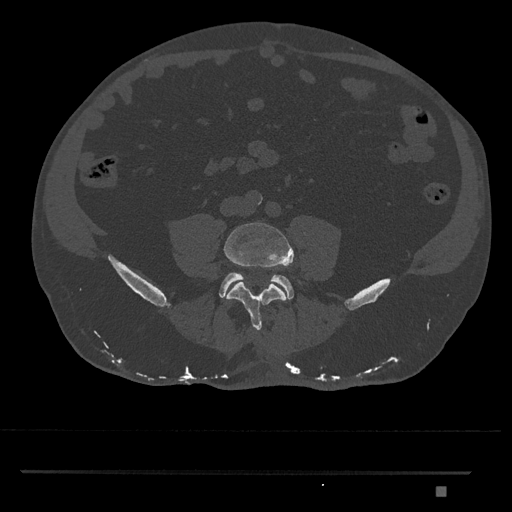
CT including the spine, one axial slice. Bone window (W 1800 / L 400 HU). 0.5 mm slice thickness. 512 × 512 image matrix. Patient: male, 65 years. Case-level facts recorded for this patient, not image findings: primary cancer: prostate.
Structures marked on this image (semi-automatically segmented with operator editing):
- L4 vertebra: bounding box <224,222,294,331> (left, top, right, bottom; pixels)
- L5 vertebra: <219,272,294,299>